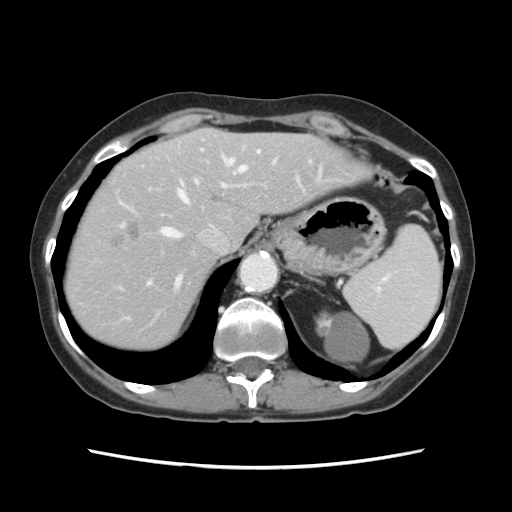
Contrast-enhanced abdominal CT, one axial slice; intravenous contrast given; soft-tissue window (W 400 / L 40 HU); 512 × 512 image matrix. Female patient, age 70 years. Case-level facts recorded for this patient, not image findings: diagnosis: colorectal cancer liver metastases, imaged before liver resection; multiple liver metastases: no; largest metastasis: 2.5 cm; disease in both lobes: no.
Structures marked on this image (expert manual segmentation):
- hepatic veins: bounding box (x1, y1, x2, y2) in pixels: (162, 157, 246, 291)
- liver: (66, 129, 364, 349)
- planned liver remnant (the part of the liver to remain after resection): (132, 129, 364, 281)
- portal vein (with intrahepatic branches): (122, 150, 260, 286)
- liver metastasis: (129, 224, 140, 239)